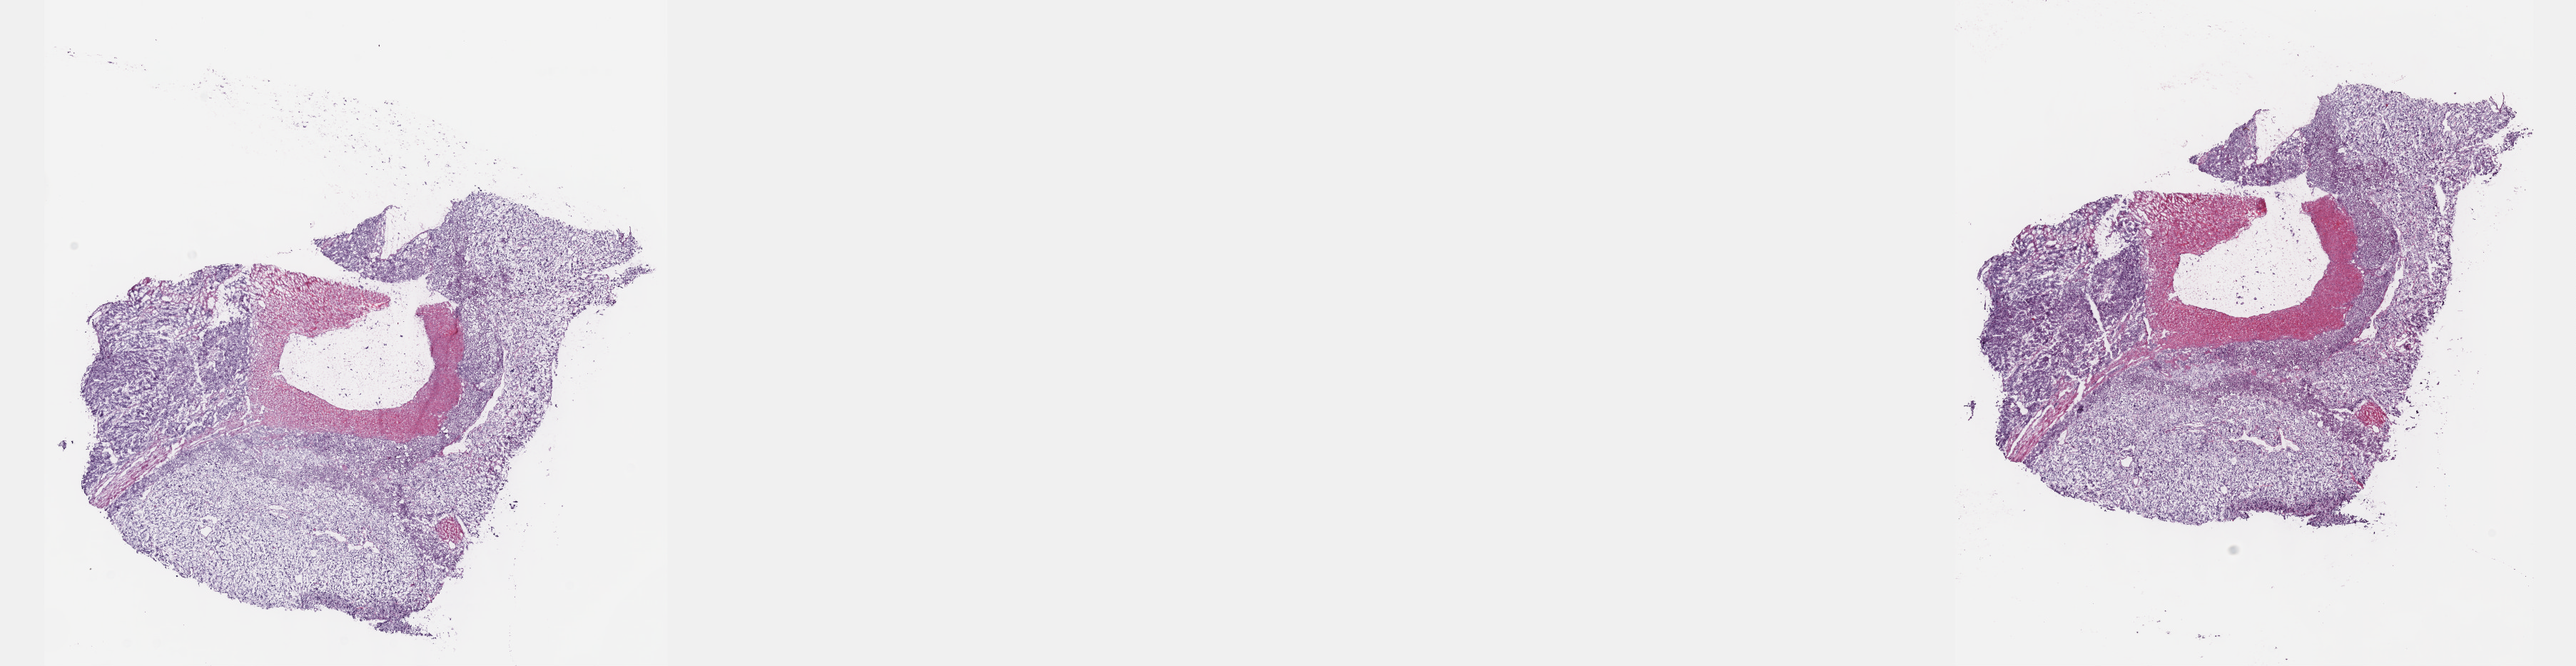
Whole-slide histology image, H&E — shown as a low-resolution overview of the whole scanned area (about 29.2 x 7.5 mm, slide scanned at 40x); frozen section from the top of the tissue portion; sample: primary tumour, adrenal gland. Female, age 76 years at initial diagnosis. Slide review estimates, as recorded: tumour cells 80%, tumour nuclei 98%, normal cells 0%, stromal cells 20%, necrosis 0%. Inflammatory infiltration, as recorded: lymphocyte infiltration 0%, monocyte infiltration 0%, neutrophil infiltration 0%.
Histologic diagnosis: Pheochromocytoma, NOS. Laterality: right.